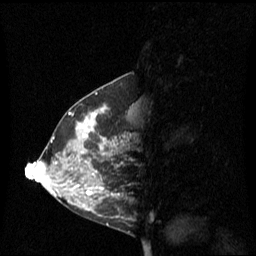
Breast MRI (dynamic contrast-enhanced), one sagittal slice. Position 28 of 60 along the scan axis. Dynamic contrast-enhanced series, image 2 of 3 at this slice position (ordered by acquisition). 1.5 T. TE 4.2 ms, TR 8.4 ms. 2.1 mm slice thickness. 256 × 256 image matrix, field of view 240 × 240 mm. Female patient, age 42 years. From the clinical record (not read from this slice): setting: breast cancer imaged before/during neoadjuvant chemotherapy; receptor status: HR-positive, HER2-negative.
Annotated regions visible in this slice (semi-automatically segmented with operator editing):
- analysis volume of interest (the breast-tissue region the enhancement analysis was run in; not a lesion): bounding box <68,106,133,201> (left, top, right, bottom; pixels)
- tumour enhancement mask (voxels above the 70 % enhancement threshold inside the analysis volume of interest): <80,110,119,197>